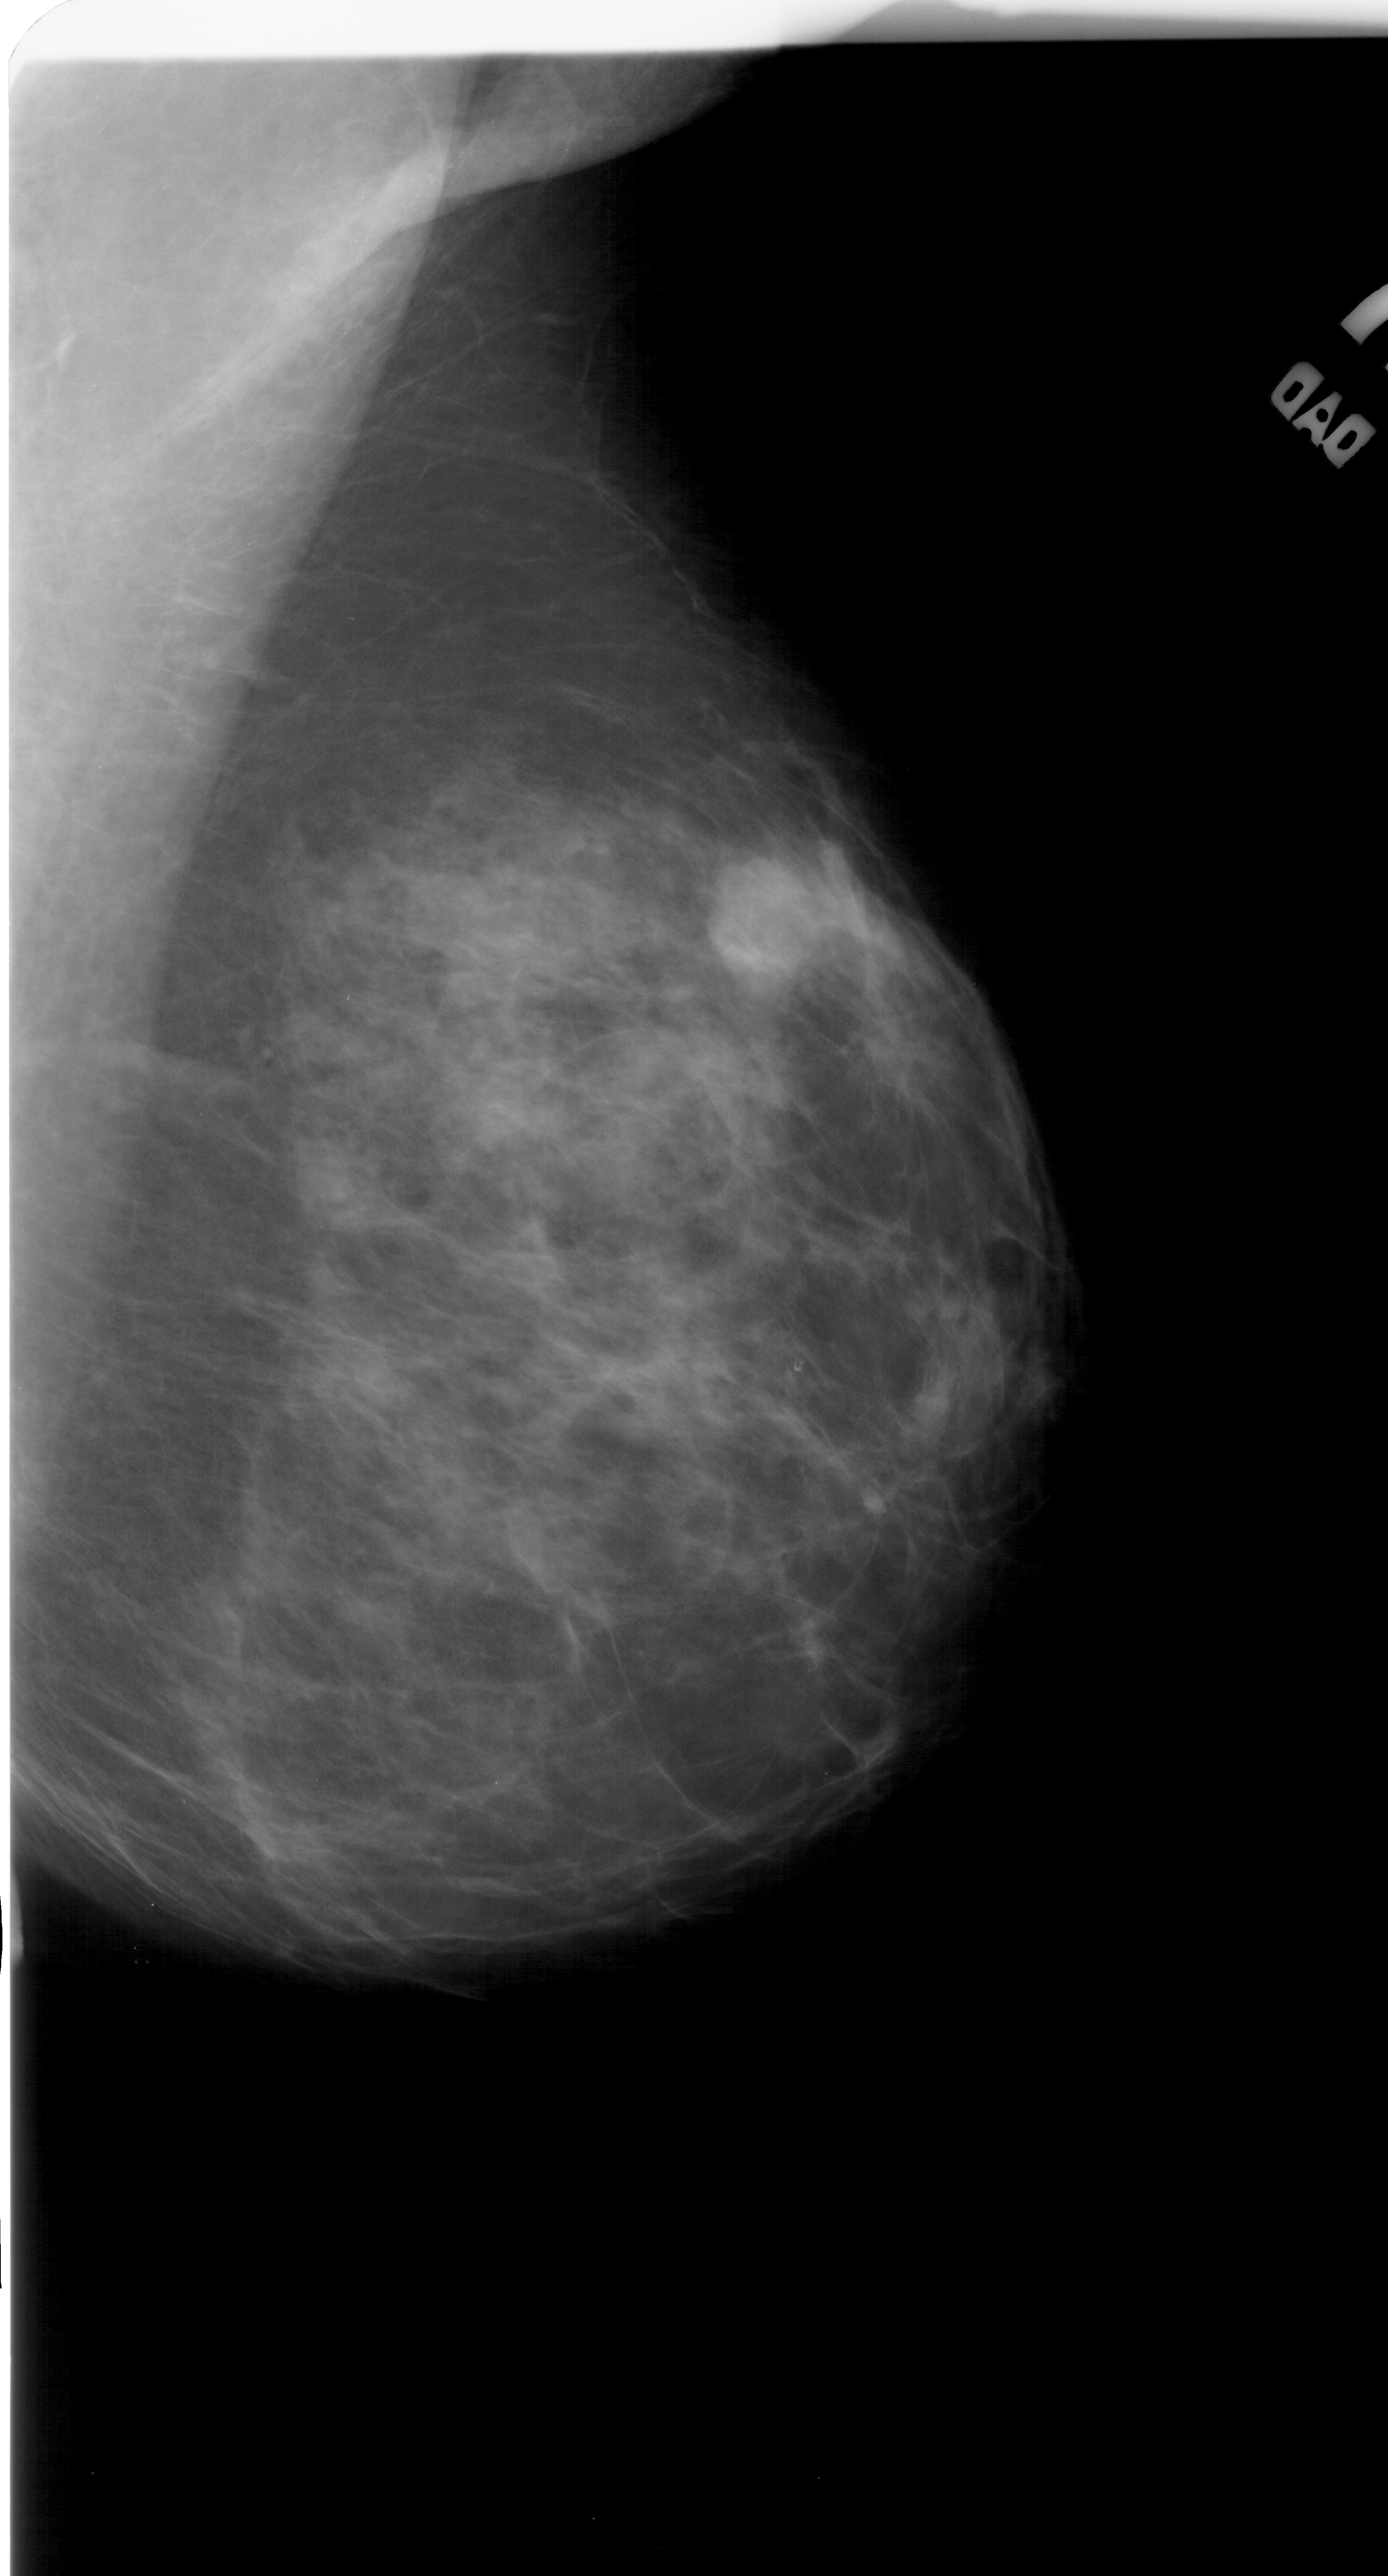
Scanned film-screen mammogram; right breast; MLO view; BI-RADS breast density category 3 (scale 1–4).
Abnormality record for this image: mass, shape lobulated, margins ill defined; BI-RADS assessment category 4; pathology result (as recorded, not read from the image): benign.